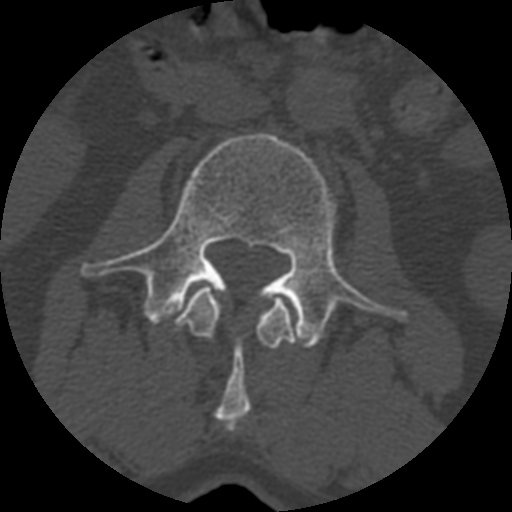
CT including the spine, one axial slice; slice 314 of 399 in the series (ordered by position); 120 kVp; bone window (W 1800 / L 400 HU); 512 × 512 image matrix. Patient age 71 years. Case-level facts recorded for this patient, not image findings: primary cancer: prostate.
Outlined on this slice (semi-automatic segmentation, software-assisted and operator-edited):
- L2 vertebra: bounding box (x1, y1, x2, y2) in pixels: (175, 286, 294, 430)
- L3 vertebra: (80, 132, 406, 348)